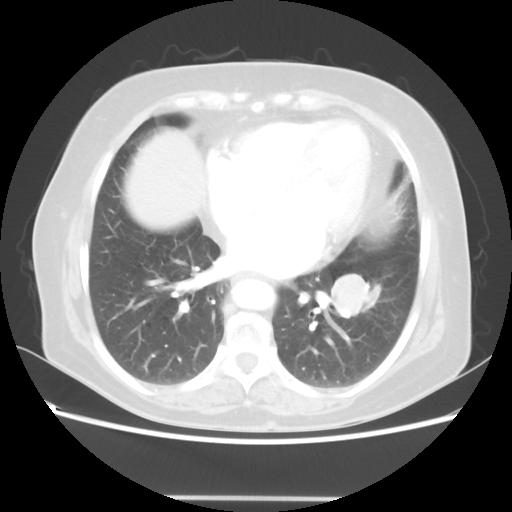
Chest CT, one axial slice. Position 22 of 56 along the scan axis. Lung window (W 1500 / L -600 HU). 512 × 512 image matrix, field of view 360 × 360 mm. Female patient, age 73 years. Case-level facts recorded for this patient, not image findings: clinical TNM (as recorded): T1c N0 M0.
Annotated regions visible in this slice (rectangle marked by the reading radiologist):
- lung tumour (recorded histology: adenocarcinoma): bounding box <328,269,374,330> (left, top, right, bottom; pixels)